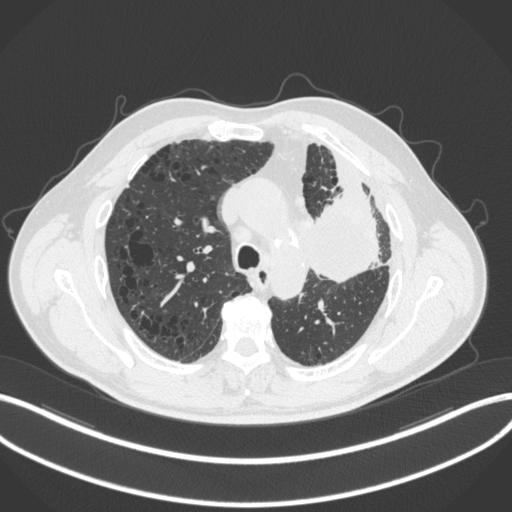
Chest CT, one axial slice. Slice 206 of 286 in the series (ordered by position). Reconstruction kernel B31f. Lung window (W 1500 / L -600 HU). 1 mm slice thickness. 512 × 512 image matrix. Patient: male, 68 years. From the clinical record (not read from this slice): clinical TNM (as recorded): T3 N3 M1.
Annotated regions visible in this slice (bounding box drawn by a radiologist):
- lung tumour (recorded histology: adenocarcinoma): bounding box [x1, y1, x2, y2] px = [310, 180, 383, 289]